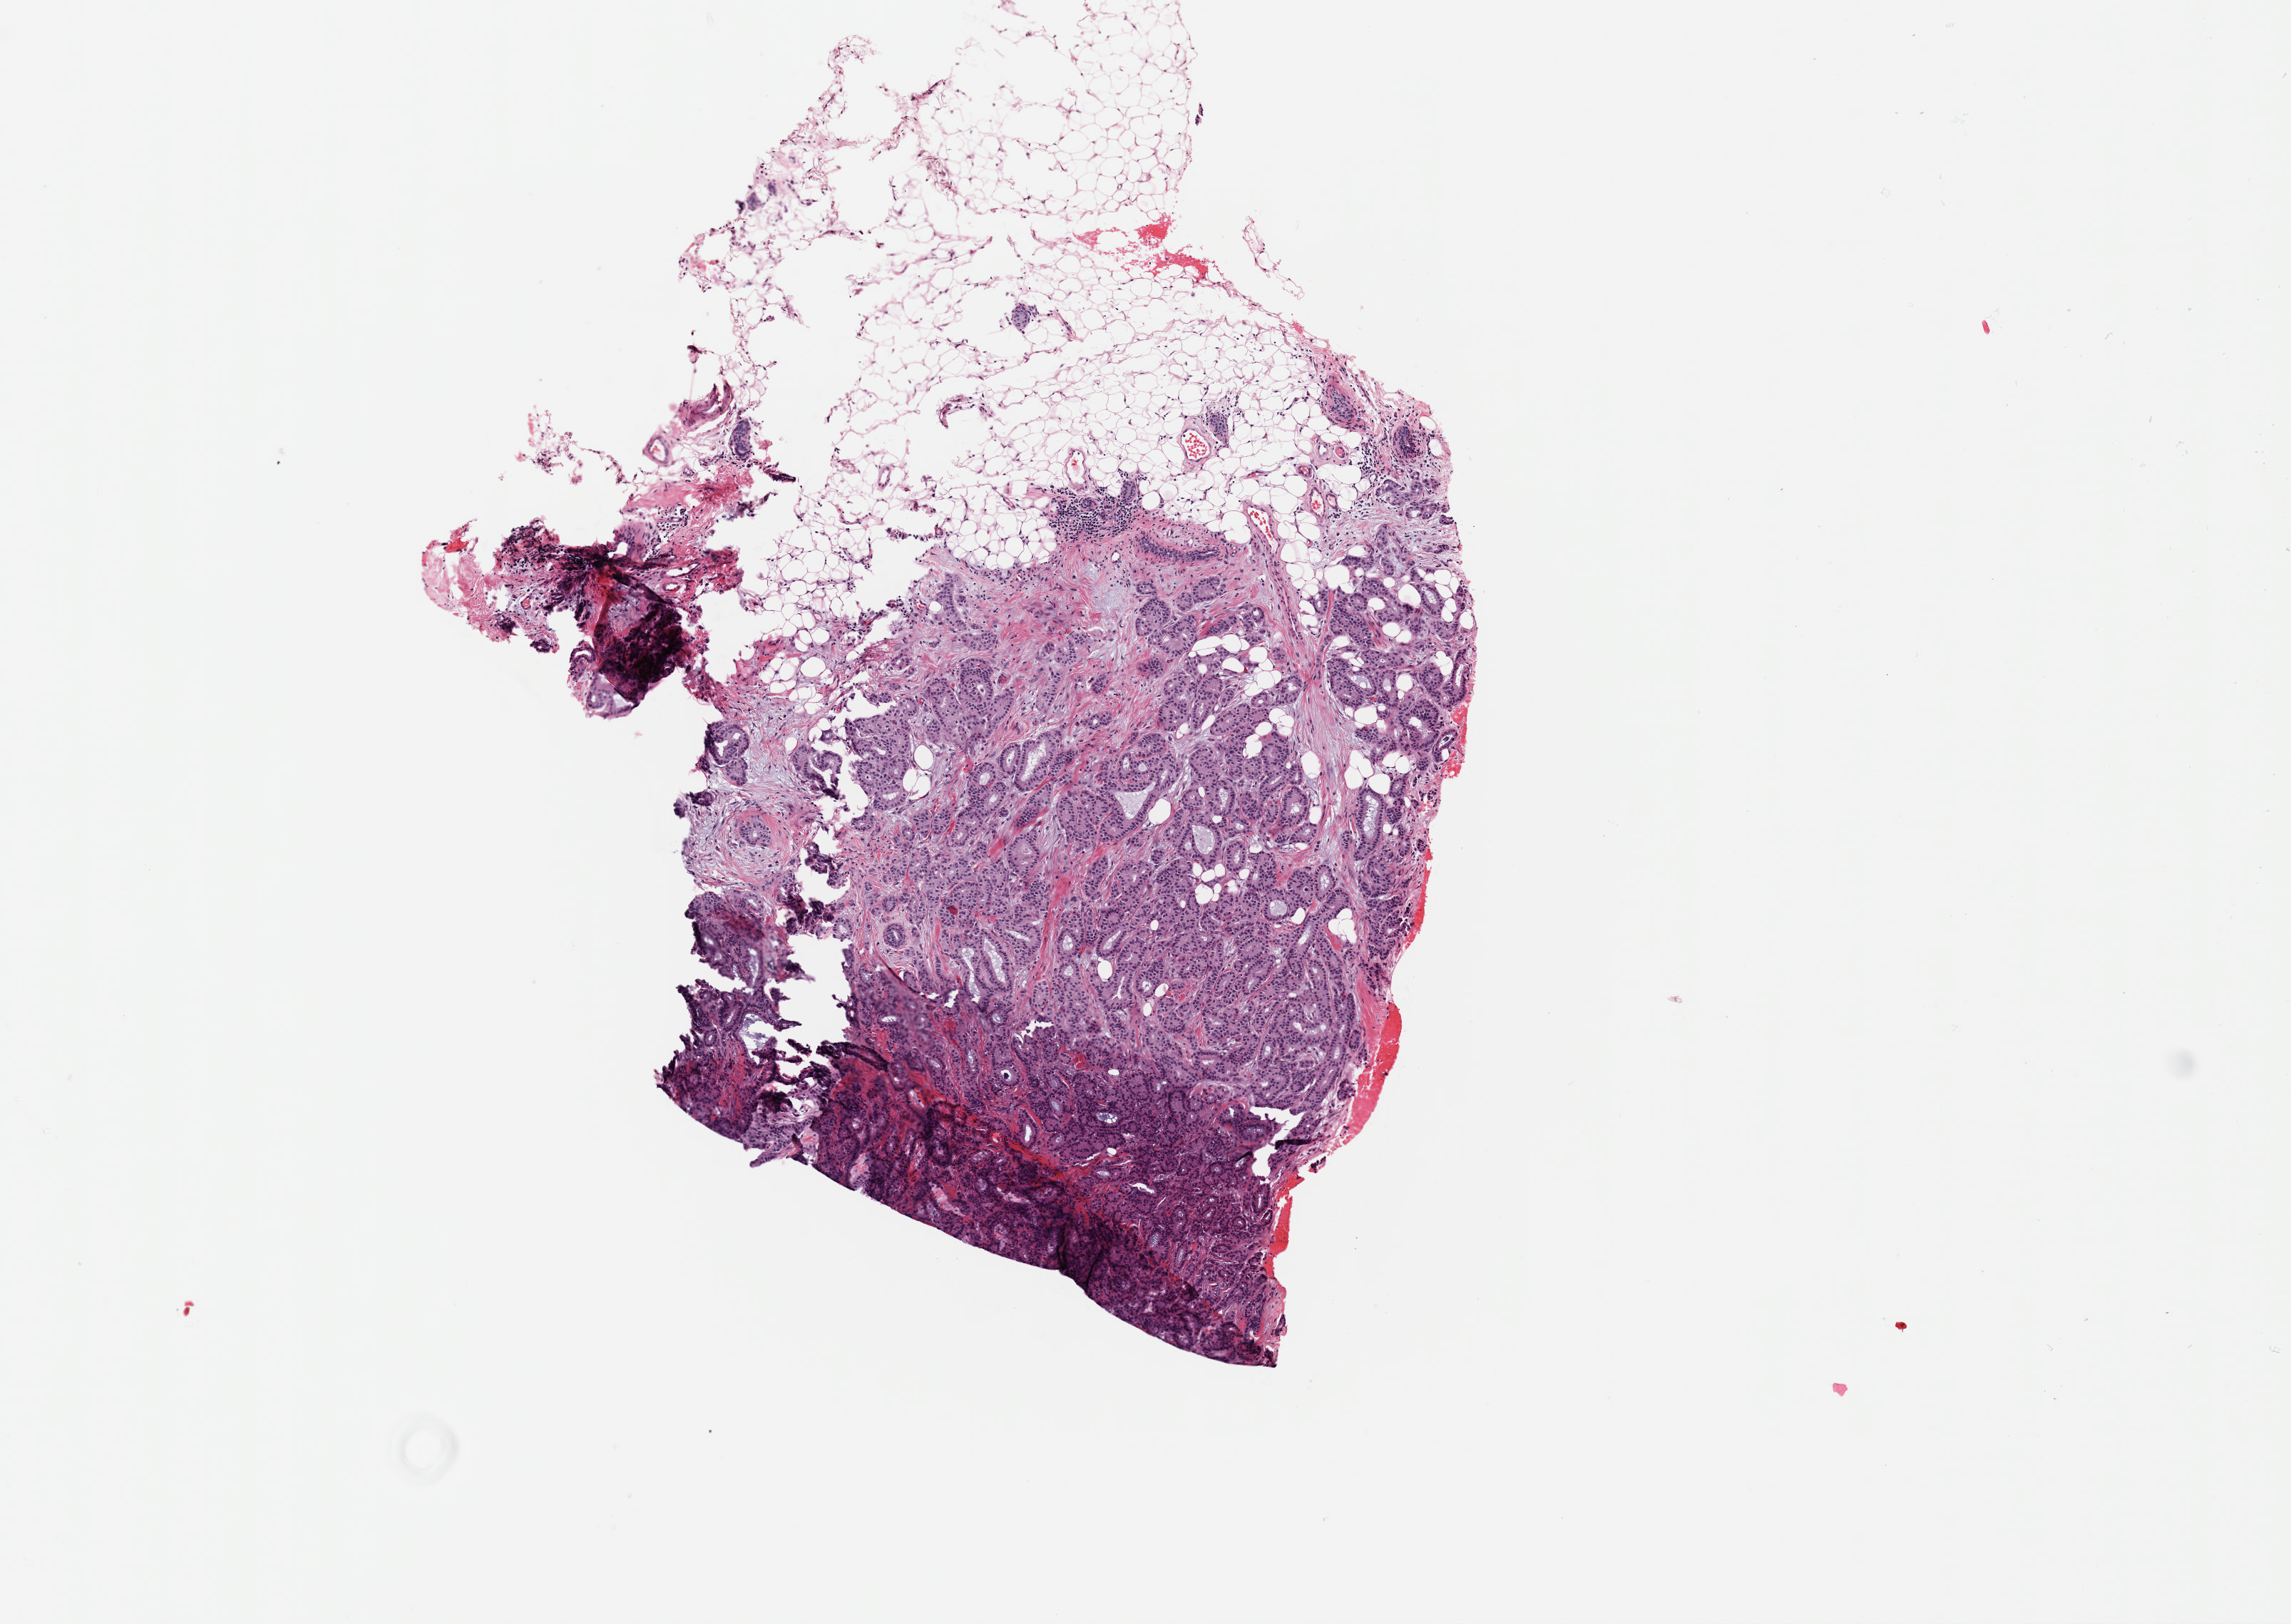
Digitized H&E-stained tissue section (whole slide) — a low-resolution overview of the entire scanned area, about 6.3 x 4.5 mm, frozen section, sample: primary tumour, breast. Female, age 79 years at initial diagnosis. Composition of this section per pathologist review: tumour cells 53%, tumour nuclei 85%, normal cells 7%, stromal cells 40%, necrosis 0%. Inflammatory infiltration, as recorded: lymphocyte infiltration 2%, monocyte infiltration 0%, neutrophil infiltration 0%.
AJCC pathologic stage: IIA (7th edition). Laterality: left. Diagnosis: Infiltrating duct carcinoma, NOS.